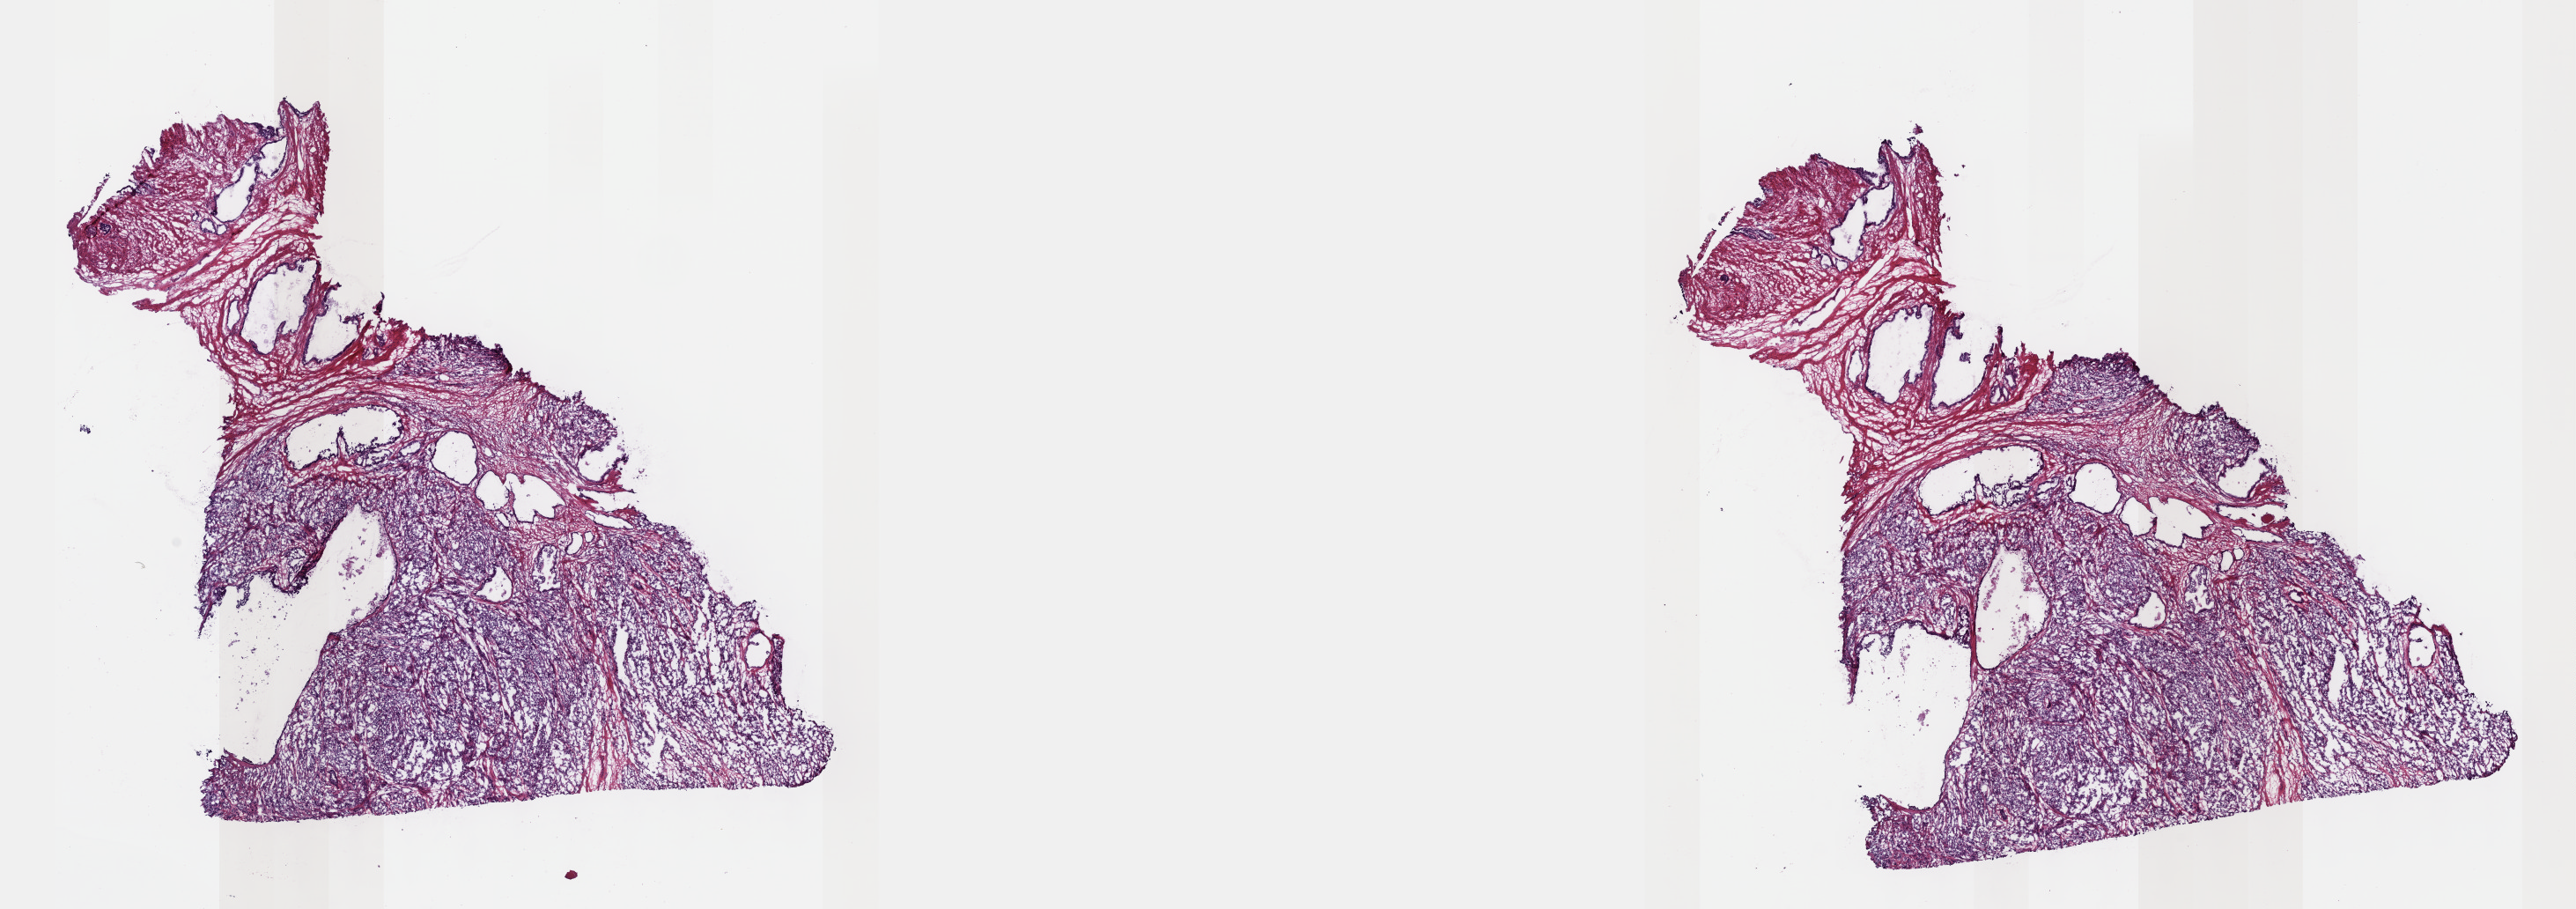
H&E-stained whole-slide image — low-resolution overview of the scanned area, about 23.6 x 8.3 mm (slide scanned at 40x), frozen section from the top of the tissue portion, primary tumour sample from the prostate. Male patient; age at initial diagnosis 73 years. Gleason score: 9 (5+4). Composition of this section per pathologist review: tumour cells 80%, tumour nuclei 80%, normal cells 3%, stromal cells 17%, necrosis 0%. Infiltration values recorded for this section: lymphocyte infiltration 3%, monocyte infiltration 1%, neutrophil infiltration 1%.
Diagnosis: Adenocarcinoma, NOS (prostate gland).